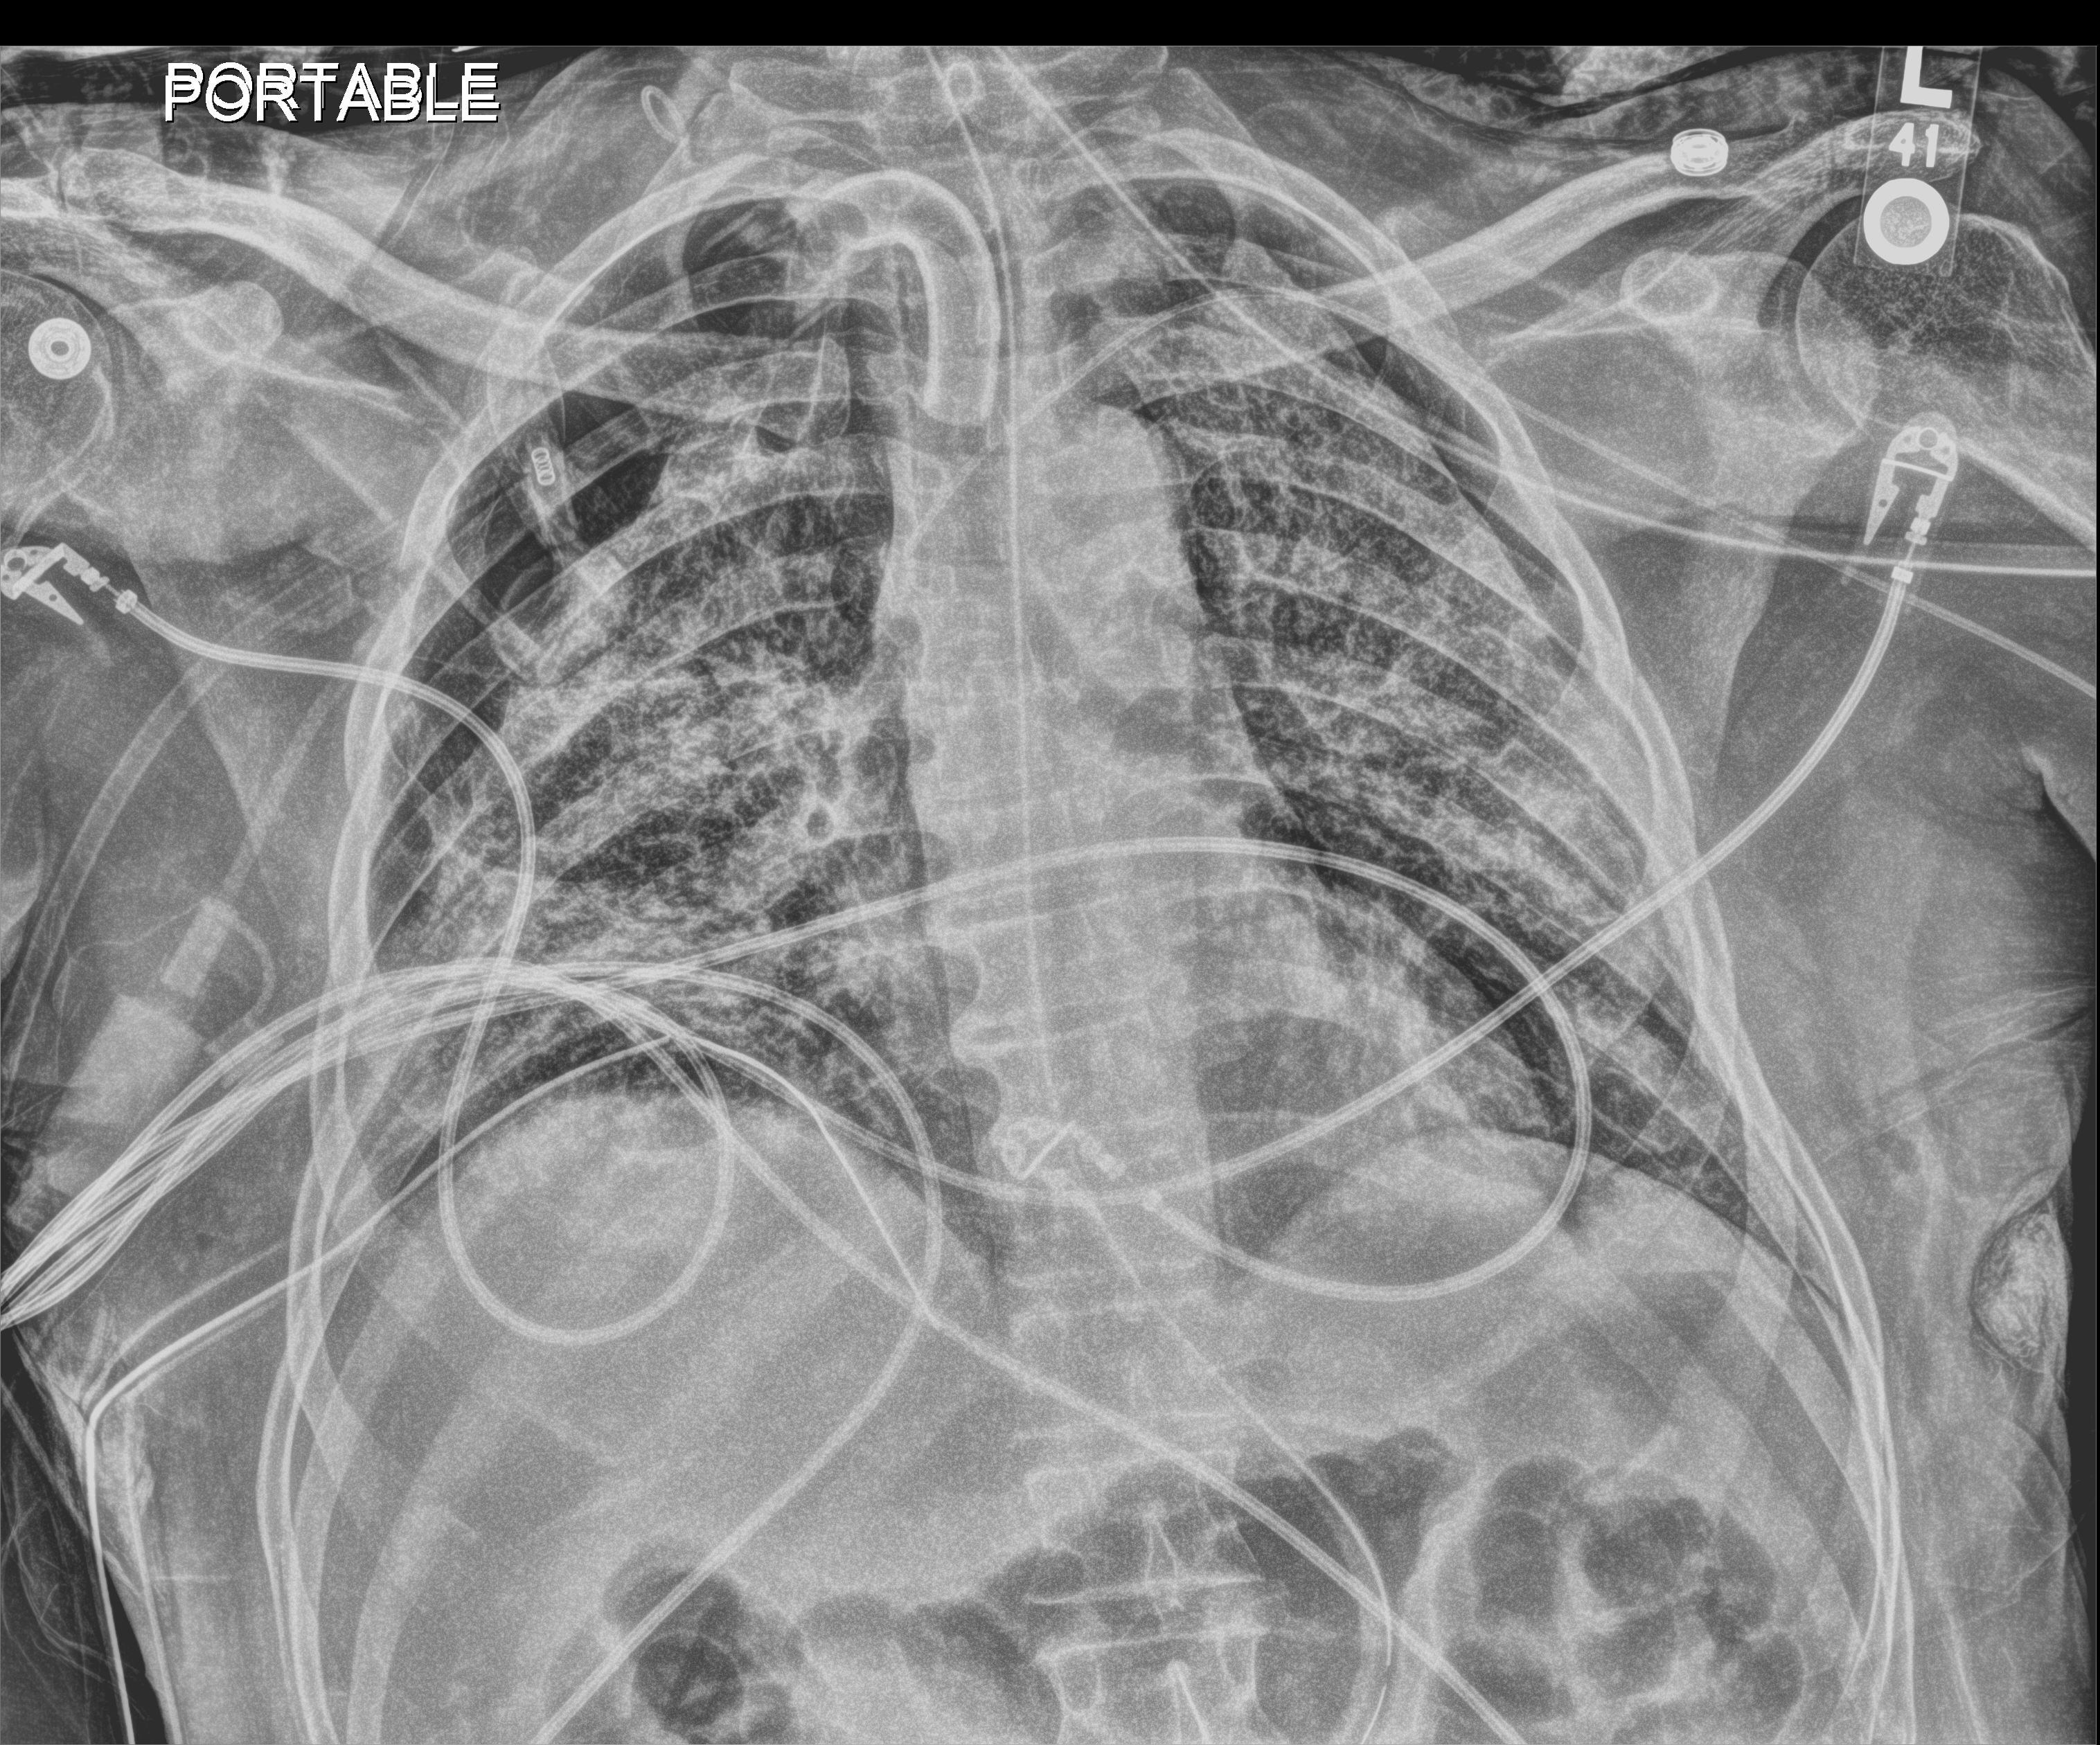
Portable chest radiograph; anteroposterior (AP) projection. Male patient hospitalised with COVID-19, age 18–59 years.
Hospital-stay facts (about this admission, not read from this image; timing relative to this image not recorded): COPD (admission record): no.